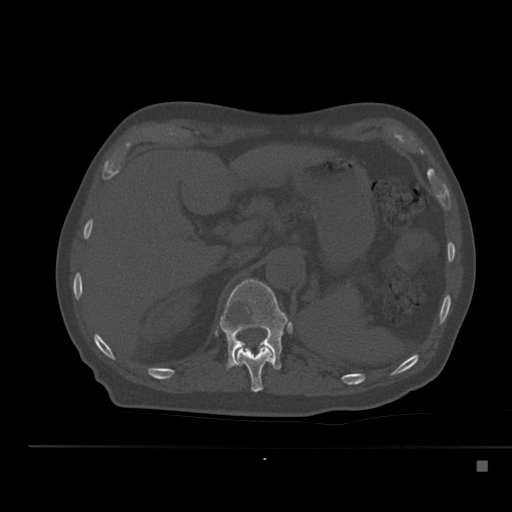
CT including the spine, one axial slice. Bone window (W 1800 / L 400 HU). 1.5 mm slice thickness. 512 × 512 image matrix, field of view 408 × 408 mm. Patient: male, 70 years. Case-level facts recorded for this patient, not image findings: primary cancer: renal; vertebrae with lytic lesions (as recorded): T4, T6, T10, T12, L3, L4, L5.
Outlined on this slice (semi-automatic segmentation, software-assisted and operator-edited):
- T11 vertebra: bounding box (x1, y1, x2, y2) in pixels: (235, 344, 274, 392)
- T12 vertebra: (219, 279, 290, 370)